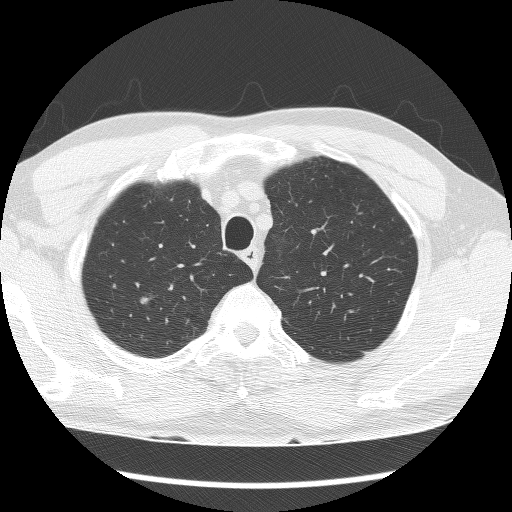
Chest CT (low-dose screening protocol), one axial image. Baseline screening round. Lung window (W 1500 / L -600 HU). 120 kVp. Slice 28 of 140 in the series. Male, age 66 years at enrolment. Current smoker at enrolment.
- Expert reader's lesion annotation, bounding box <127,287,160,316> (left, top, right, bottom; pixels).
- The screening reader recorded 2 non-calcified nodules or masses ≥4 mm on this exam (right upper lobe, right upper lobe); which of them this box marks is not recorded.
- Official screen result: positive, change unspecified: nodule(s) >= 4 mm or enlarging nodule(s), mass(es), or other non-specific abnormalities suspicious for lung cancer.